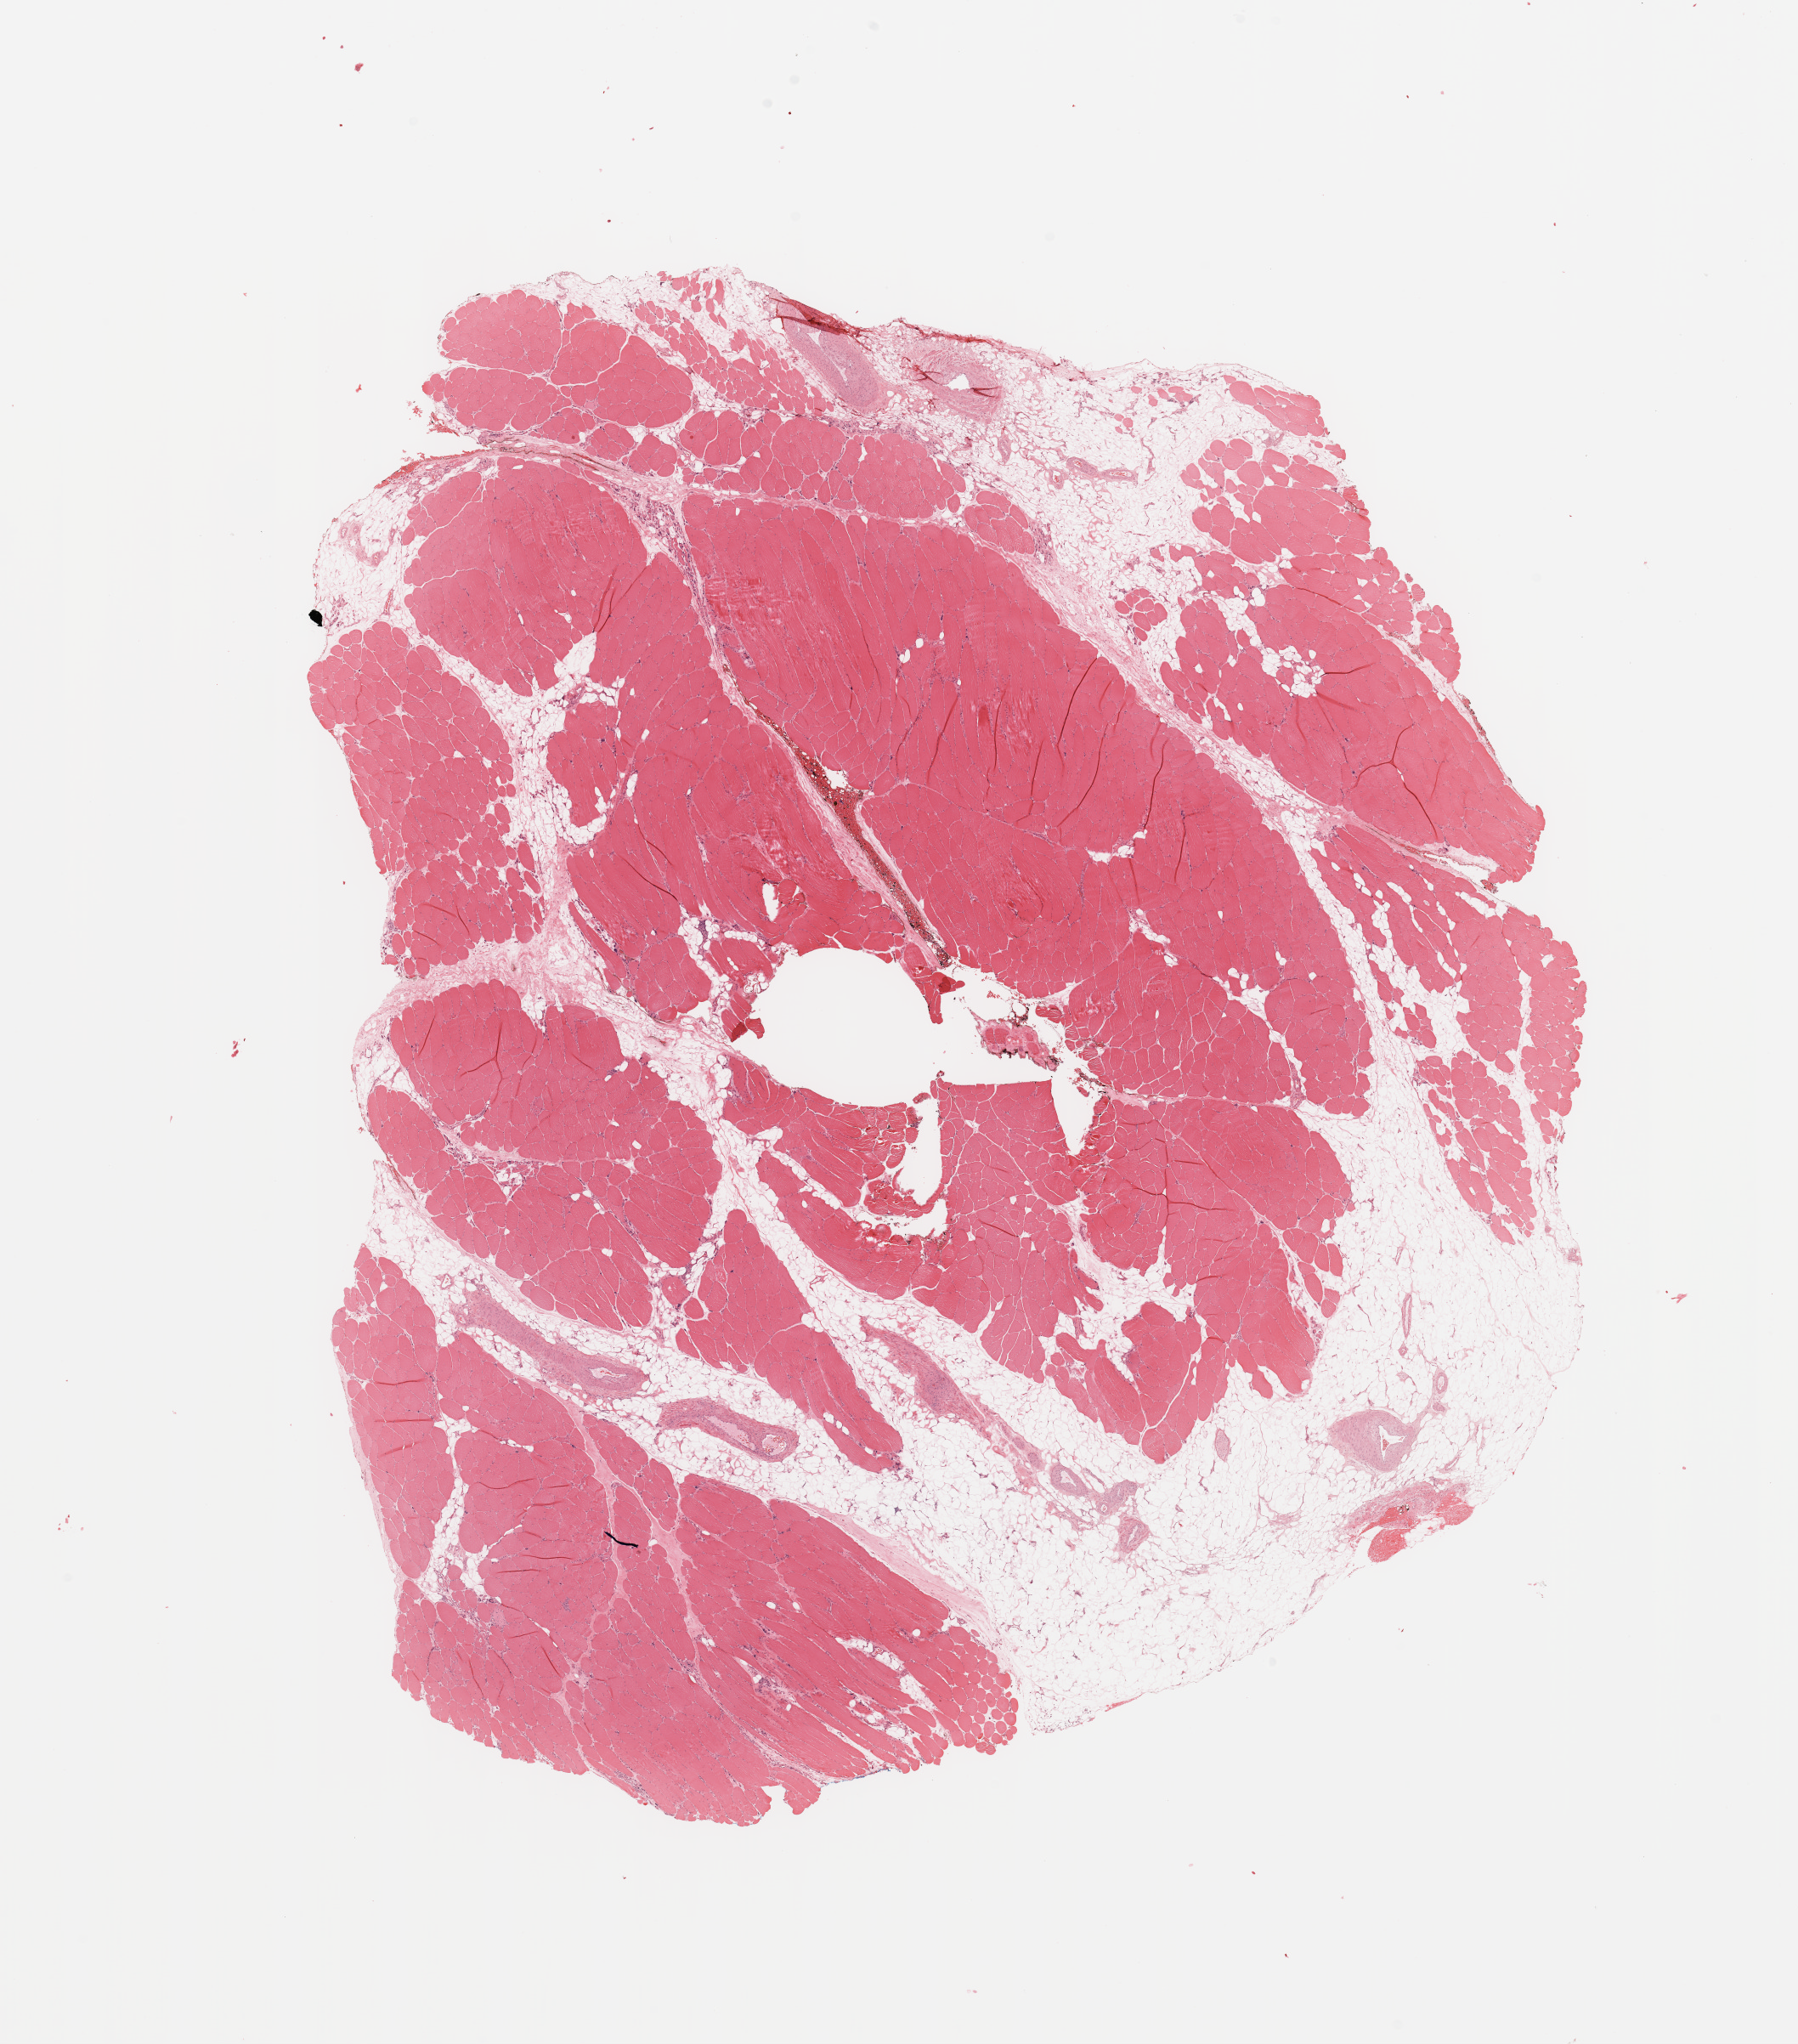
Hematoxylin and eosin (H&E) stained whole-slide image — whole scanned area (about 16.7 x 19.0 mm) shown as a low-resolution overview. Normal (non-tumour) tissue sample. 86-year-old male patient.
- this section: normal (non-tumour) tissue from the same patient
- patient diagnosis (cohort enrolment): sarcoma (site not recorded at cohort level)